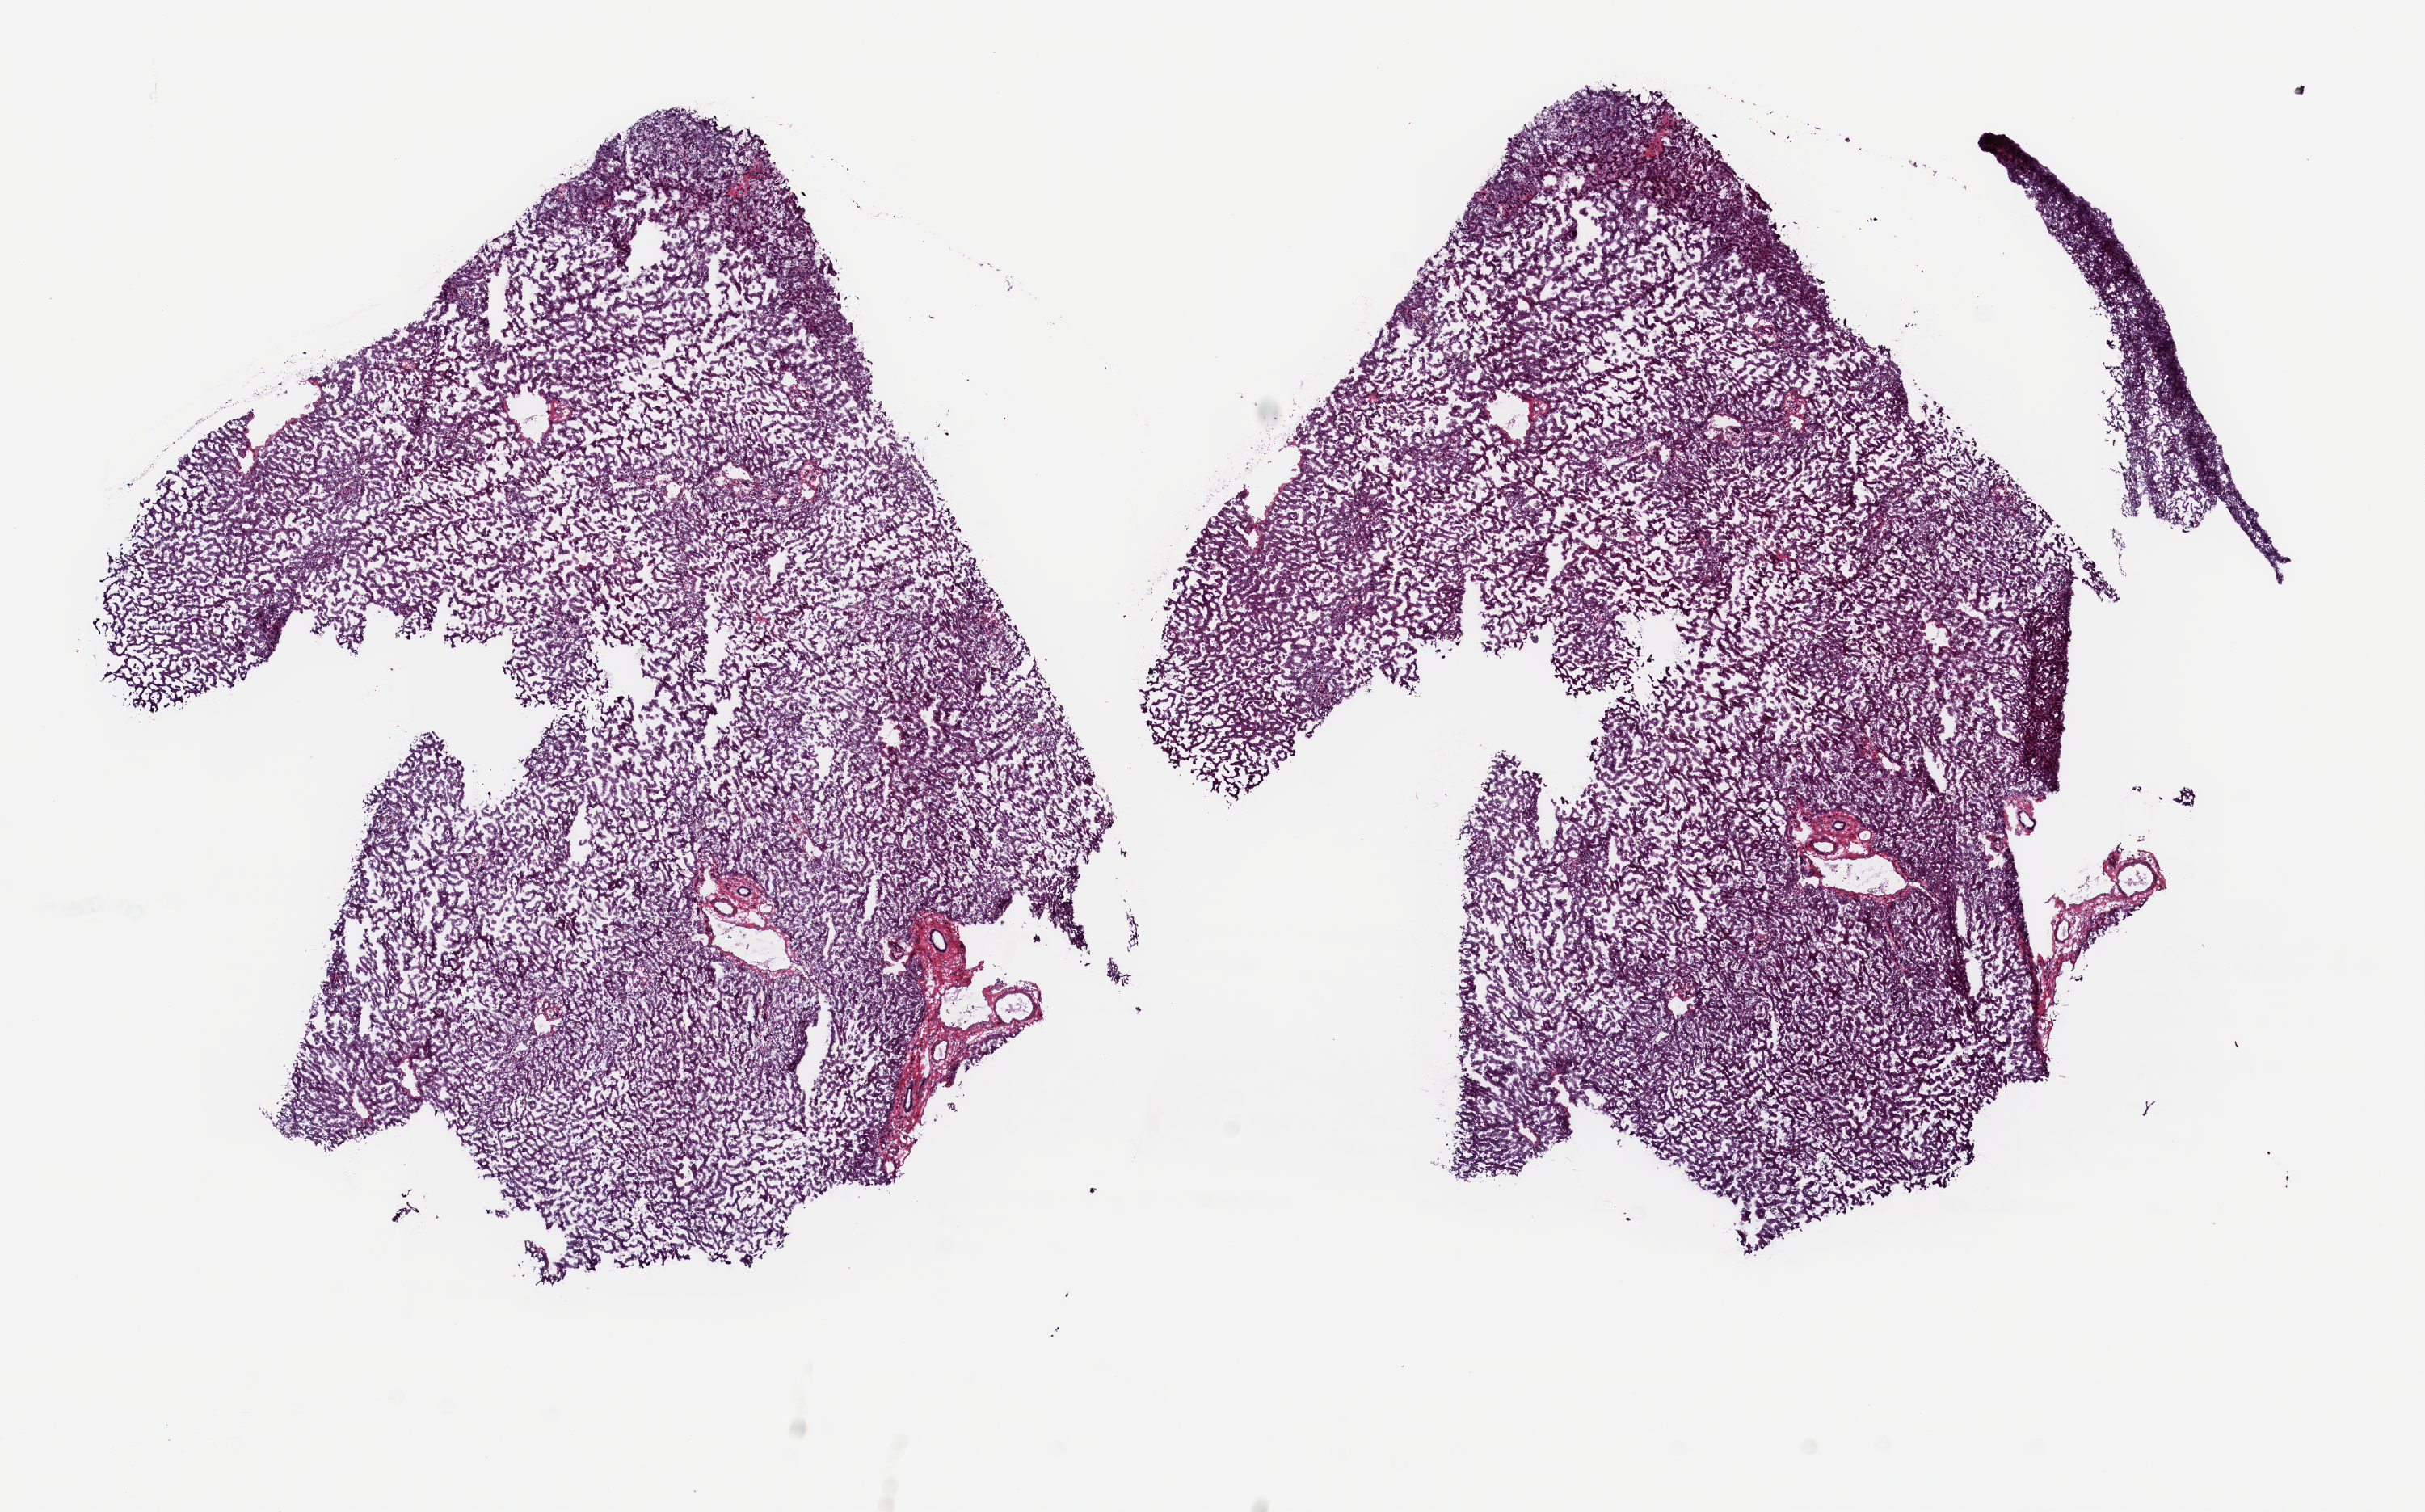
Whole-slide histology image, H&E-stained, whole scanned area (about 11.9 x 7.4 mm, from a 20x scan) shown as a low-resolution overview. Frozen section from the top of the tissue portion. Solid tissue normal (non-tumour tissue) sample from the liver. Female patient; age at initial diagnosis 20 years. Pathologist review of this section (percent, as recorded): tumour cells 0%, tumour nuclei 0%, normal cells 100%, stromal cells 0%, necrosis 0%. Inflammatory infiltration, as recorded: lymphocyte infiltration 0%, monocyte infiltration 0%, neutrophil infiltration 0%.
- this section: solid tissue normal sample (biorepository sample class)
- patient diagnosis: Hepatocellular carcinoma, NOS